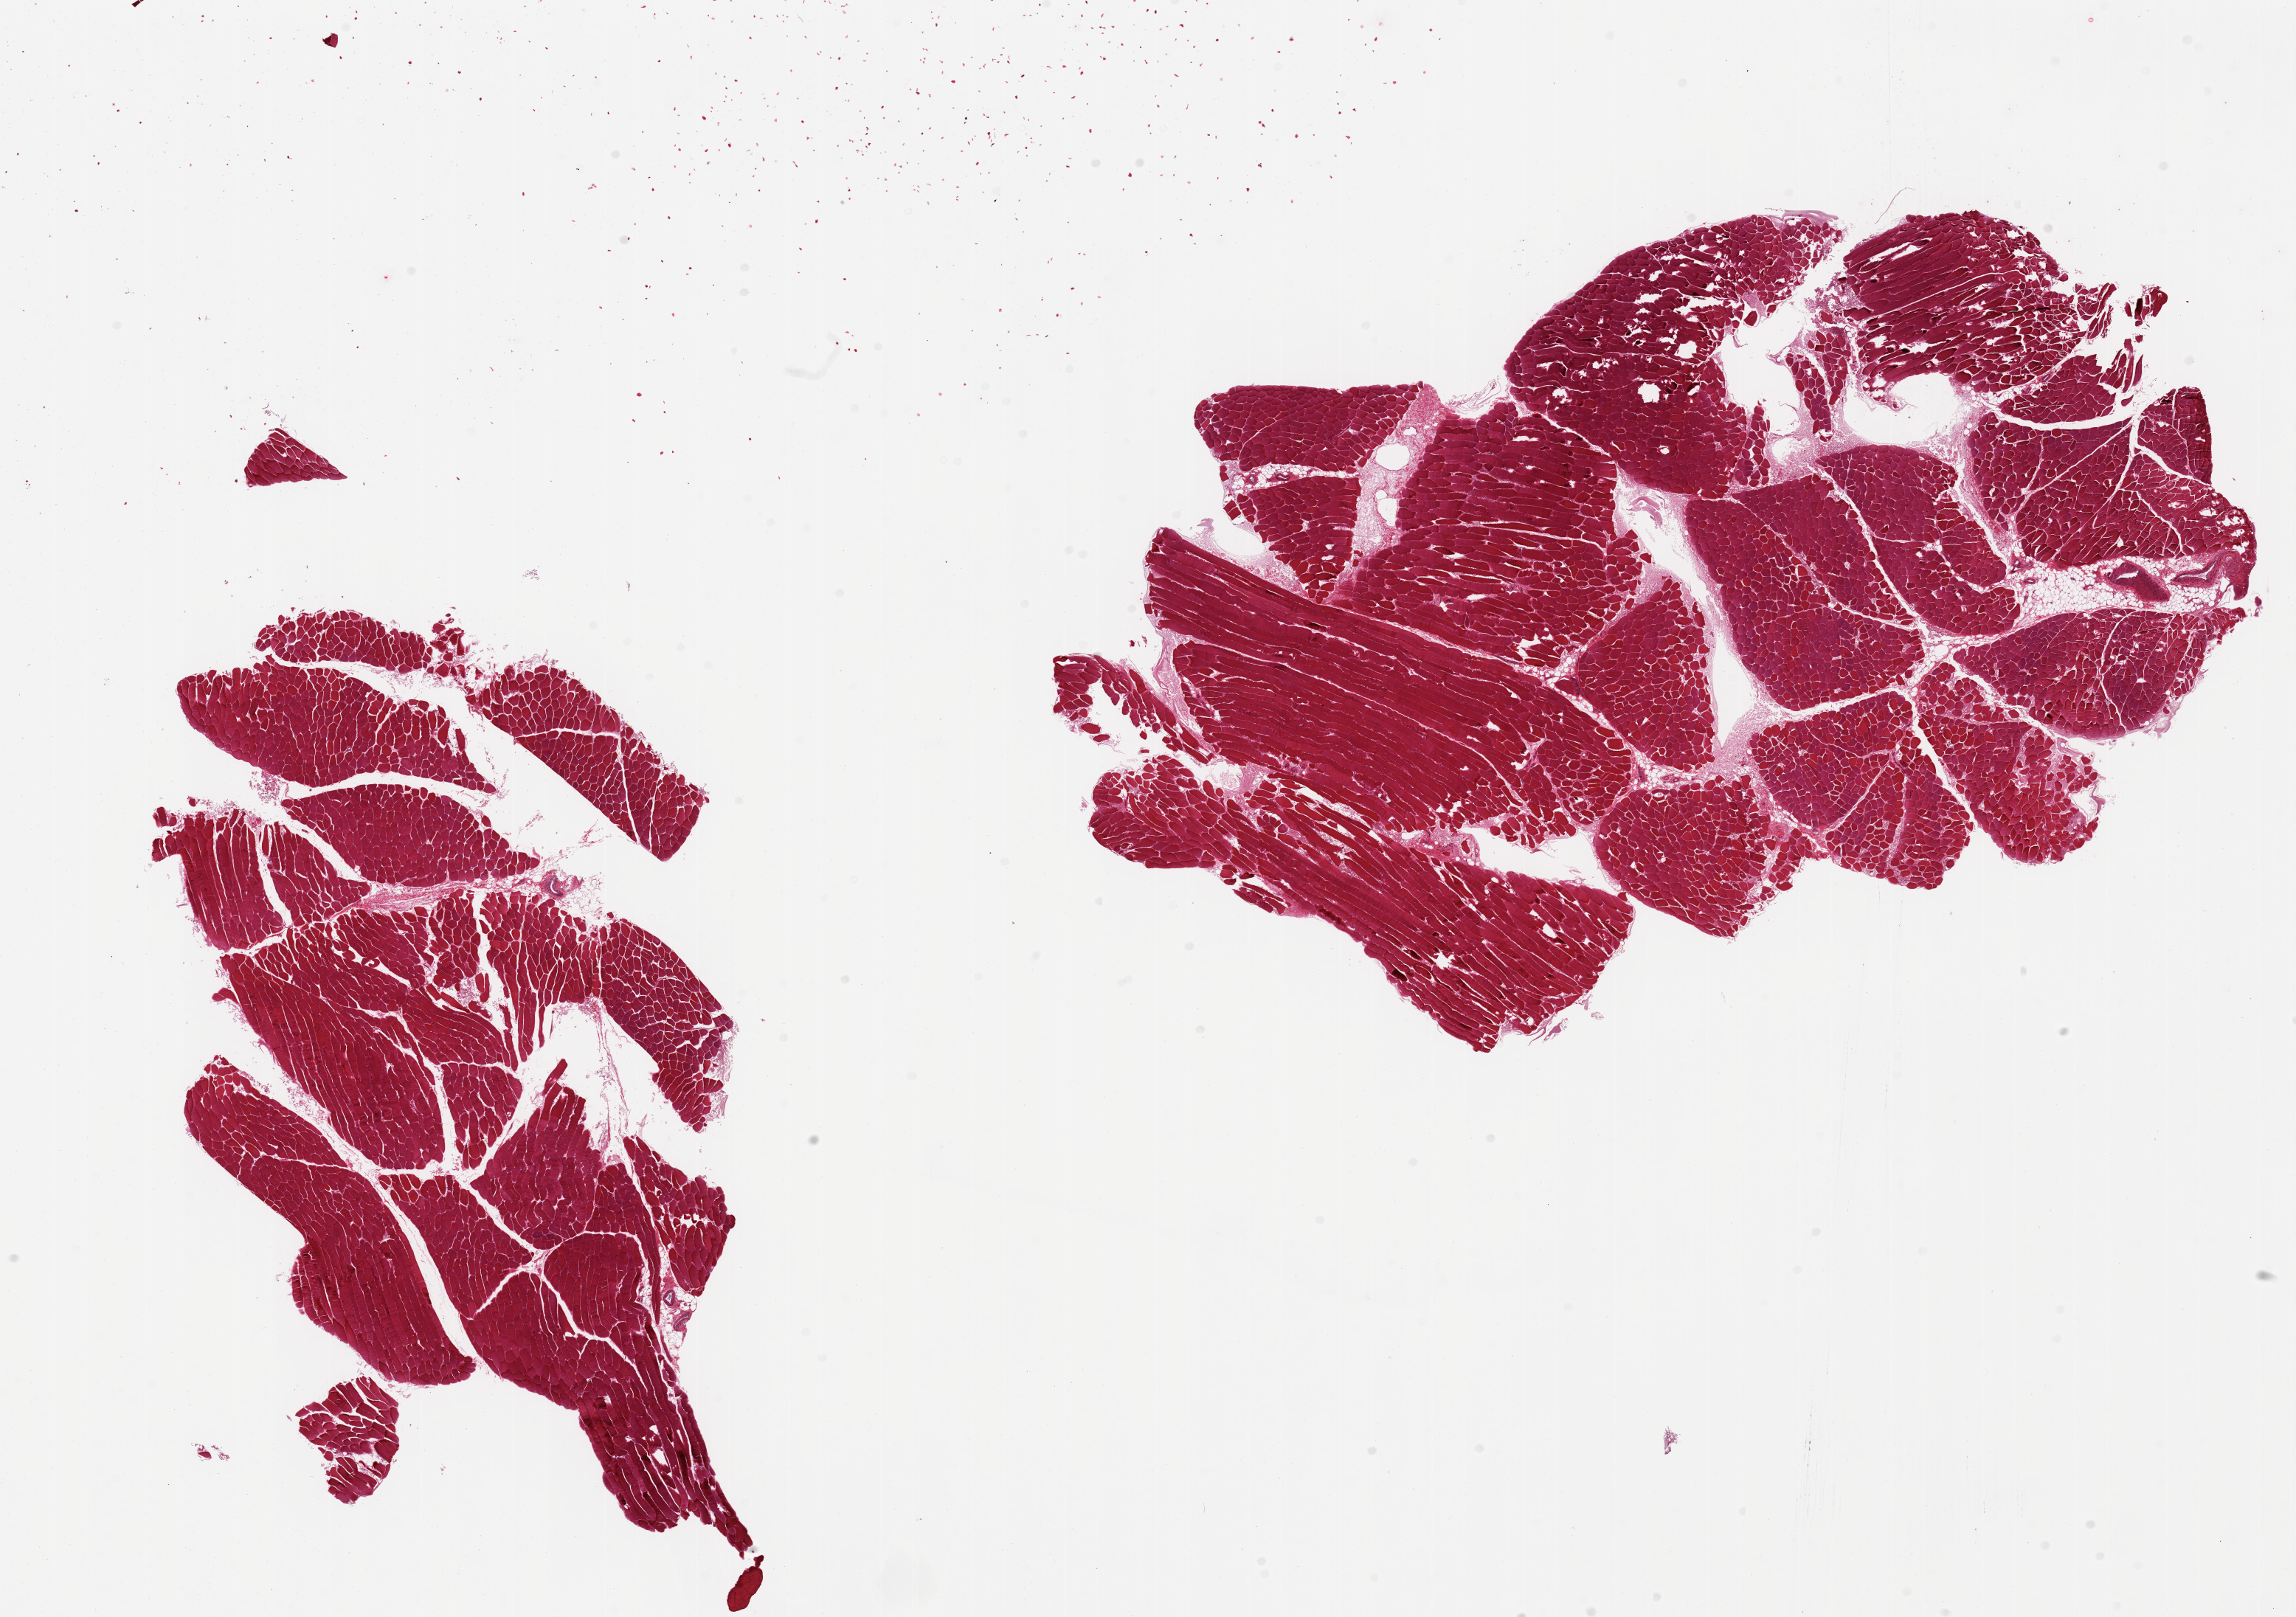
Whole-slide image, haematoxylin and eosin stain, whole scanned area (about 24.6 x 17.3 mm) shown as a low-resolution overview. PAXgene-fixed paraffin-embedded (PFPE) section. Target tissue: skeletal muscle. Donor tissue sample.
Review note (as recorded): 2 pieces; minimal internal fat.